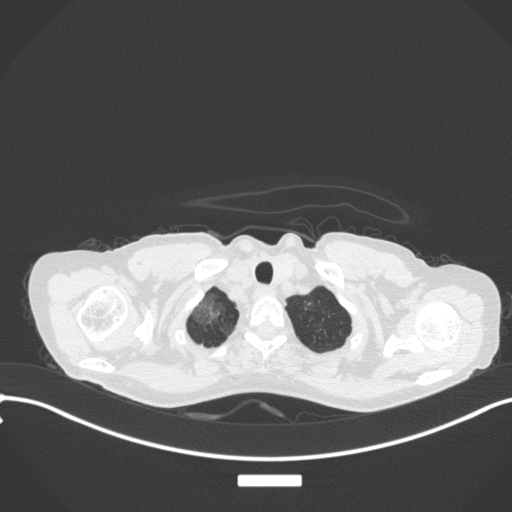
Chest CT, one axial slice. Position 310 of 311 along the scan axis. Reconstruction kernel B31f. Lung window (W 1500 / L -600 HU). 512 × 512 image matrix, field of view 400 × 400 mm. Female patient, age 59 years. From the clinical record (not read from this slice): clinical TNM (as recorded): T3 N0 M0; histopathological grade: G1.
Outlined on this slice (rectangle marked by the reading radiologist):
- lung tumour (recorded histology: adenocarcinoma): bounding box (x1, y1, x2, y2) in pixels: (189, 293, 221, 327)